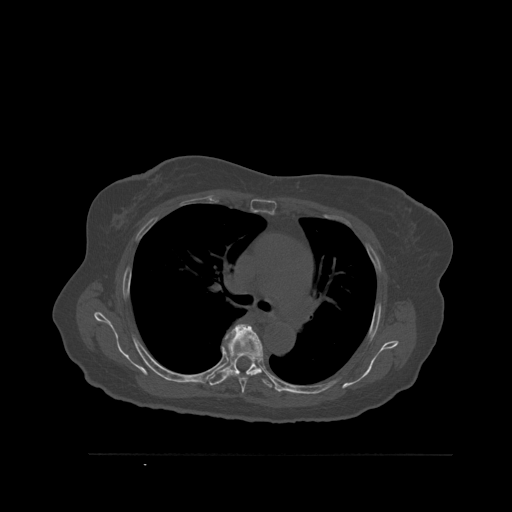
CT including the spine, one axial slice; position 388 of 527 along the scan axis; bone window (W 1800 / L 400 HU); 512 × 512 image matrix, field of view 470 × 470 mm. Patient: female, 73 years. Case-level facts recorded for this patient, not image findings: primary cancer: breast.
Structures marked on this image (semi-automatically segmented with operator editing):
- T5 vertebra: bounding box <226,324,263,394> (left, top, right, bottom; pixels)
- T6 vertebra: <207,324,273,388>